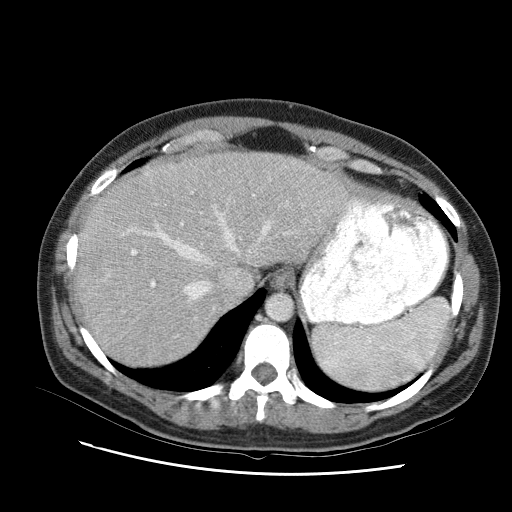
Contrast-enhanced abdominal CT (liver protocol), one axial slice. Position 74 of 95 along the scan axis. One of 2 acquisitions stored at this slice position. Soft-tissue window (W 400 / L 40 HU). 512 × 512 image matrix, field of view 360 × 360 mm. From the clinical record (not read from this slice): diagnosis: hepatocellular carcinoma (patient treated with transarterial chemoembolisation; whether this scan precedes or follows treatment is not stated here); TNM stage (as recorded): Stage-I; Child-Pugh class: B; tumour differentiation: moderately differentiated.
Outlined on this slice (semi-automatic segmentation, software-assisted and operator-edited):
- liver parenchyma outside the tumour (the mass and vessels are separate outlines, so this box may not span the whole liver): bounding box <72,148,350,348> (left, top, right, bottom; pixels)
- liver vessels: <116,167,260,322>